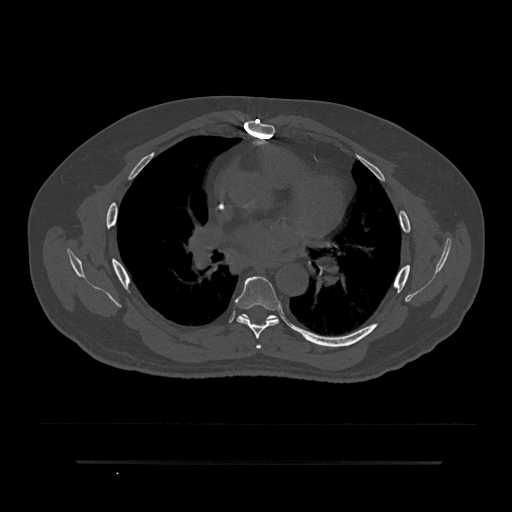
CT including the spine, one axial slice. Slice 516 of 797 in the series (ordered by position). Reconstruction kernel Br40s/3. 120 kVp. Bone window (W 1800 / L 400 HU). 0.5 mm slice thickness. 512 × 512 image matrix, field of view 464 × 464 mm. Patient: male, 59 years. From the clinical record (not read from this slice): primary cancer: bile ducts; vertebrae with lytic lesions (as recorded): T10.
Annotated regions visible in this slice (semi-automatic segmentation, software-assisted and operator-edited):
- T5 vertebra: box from (x=256, y=344) to (x=262, y=349) px
- T6 vertebra: (x=235, y=276)–(x=281, y=339)
- T7 vertebra: (x=243, y=314)–(x=274, y=318)